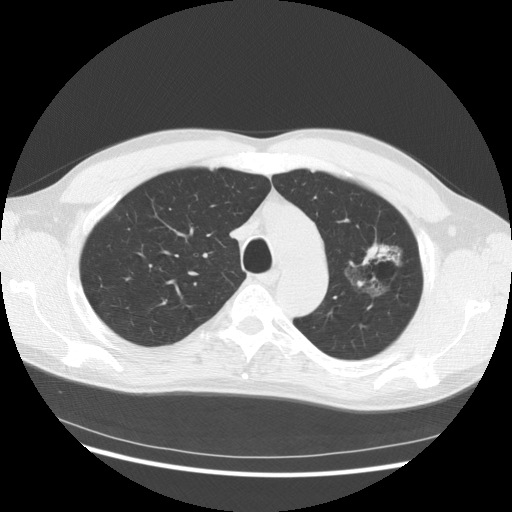
Low-dose screening chest CT, one axial slice. Position 107 of 145 along the scan axis. Reconstruction kernel STANDARD. 140 kVp. Lung window (W 1500 / L -600 HU). 2.5 mm slice thickness. 512 × 512 image matrix, field of view 370 × 370 mm.
Structures marked on this image (expert manual segmentation):
- lesion 1 (tumor, upper lobe of left lung): bounding box [x1, y1, x2, y2] px = [363, 245, 389, 264]